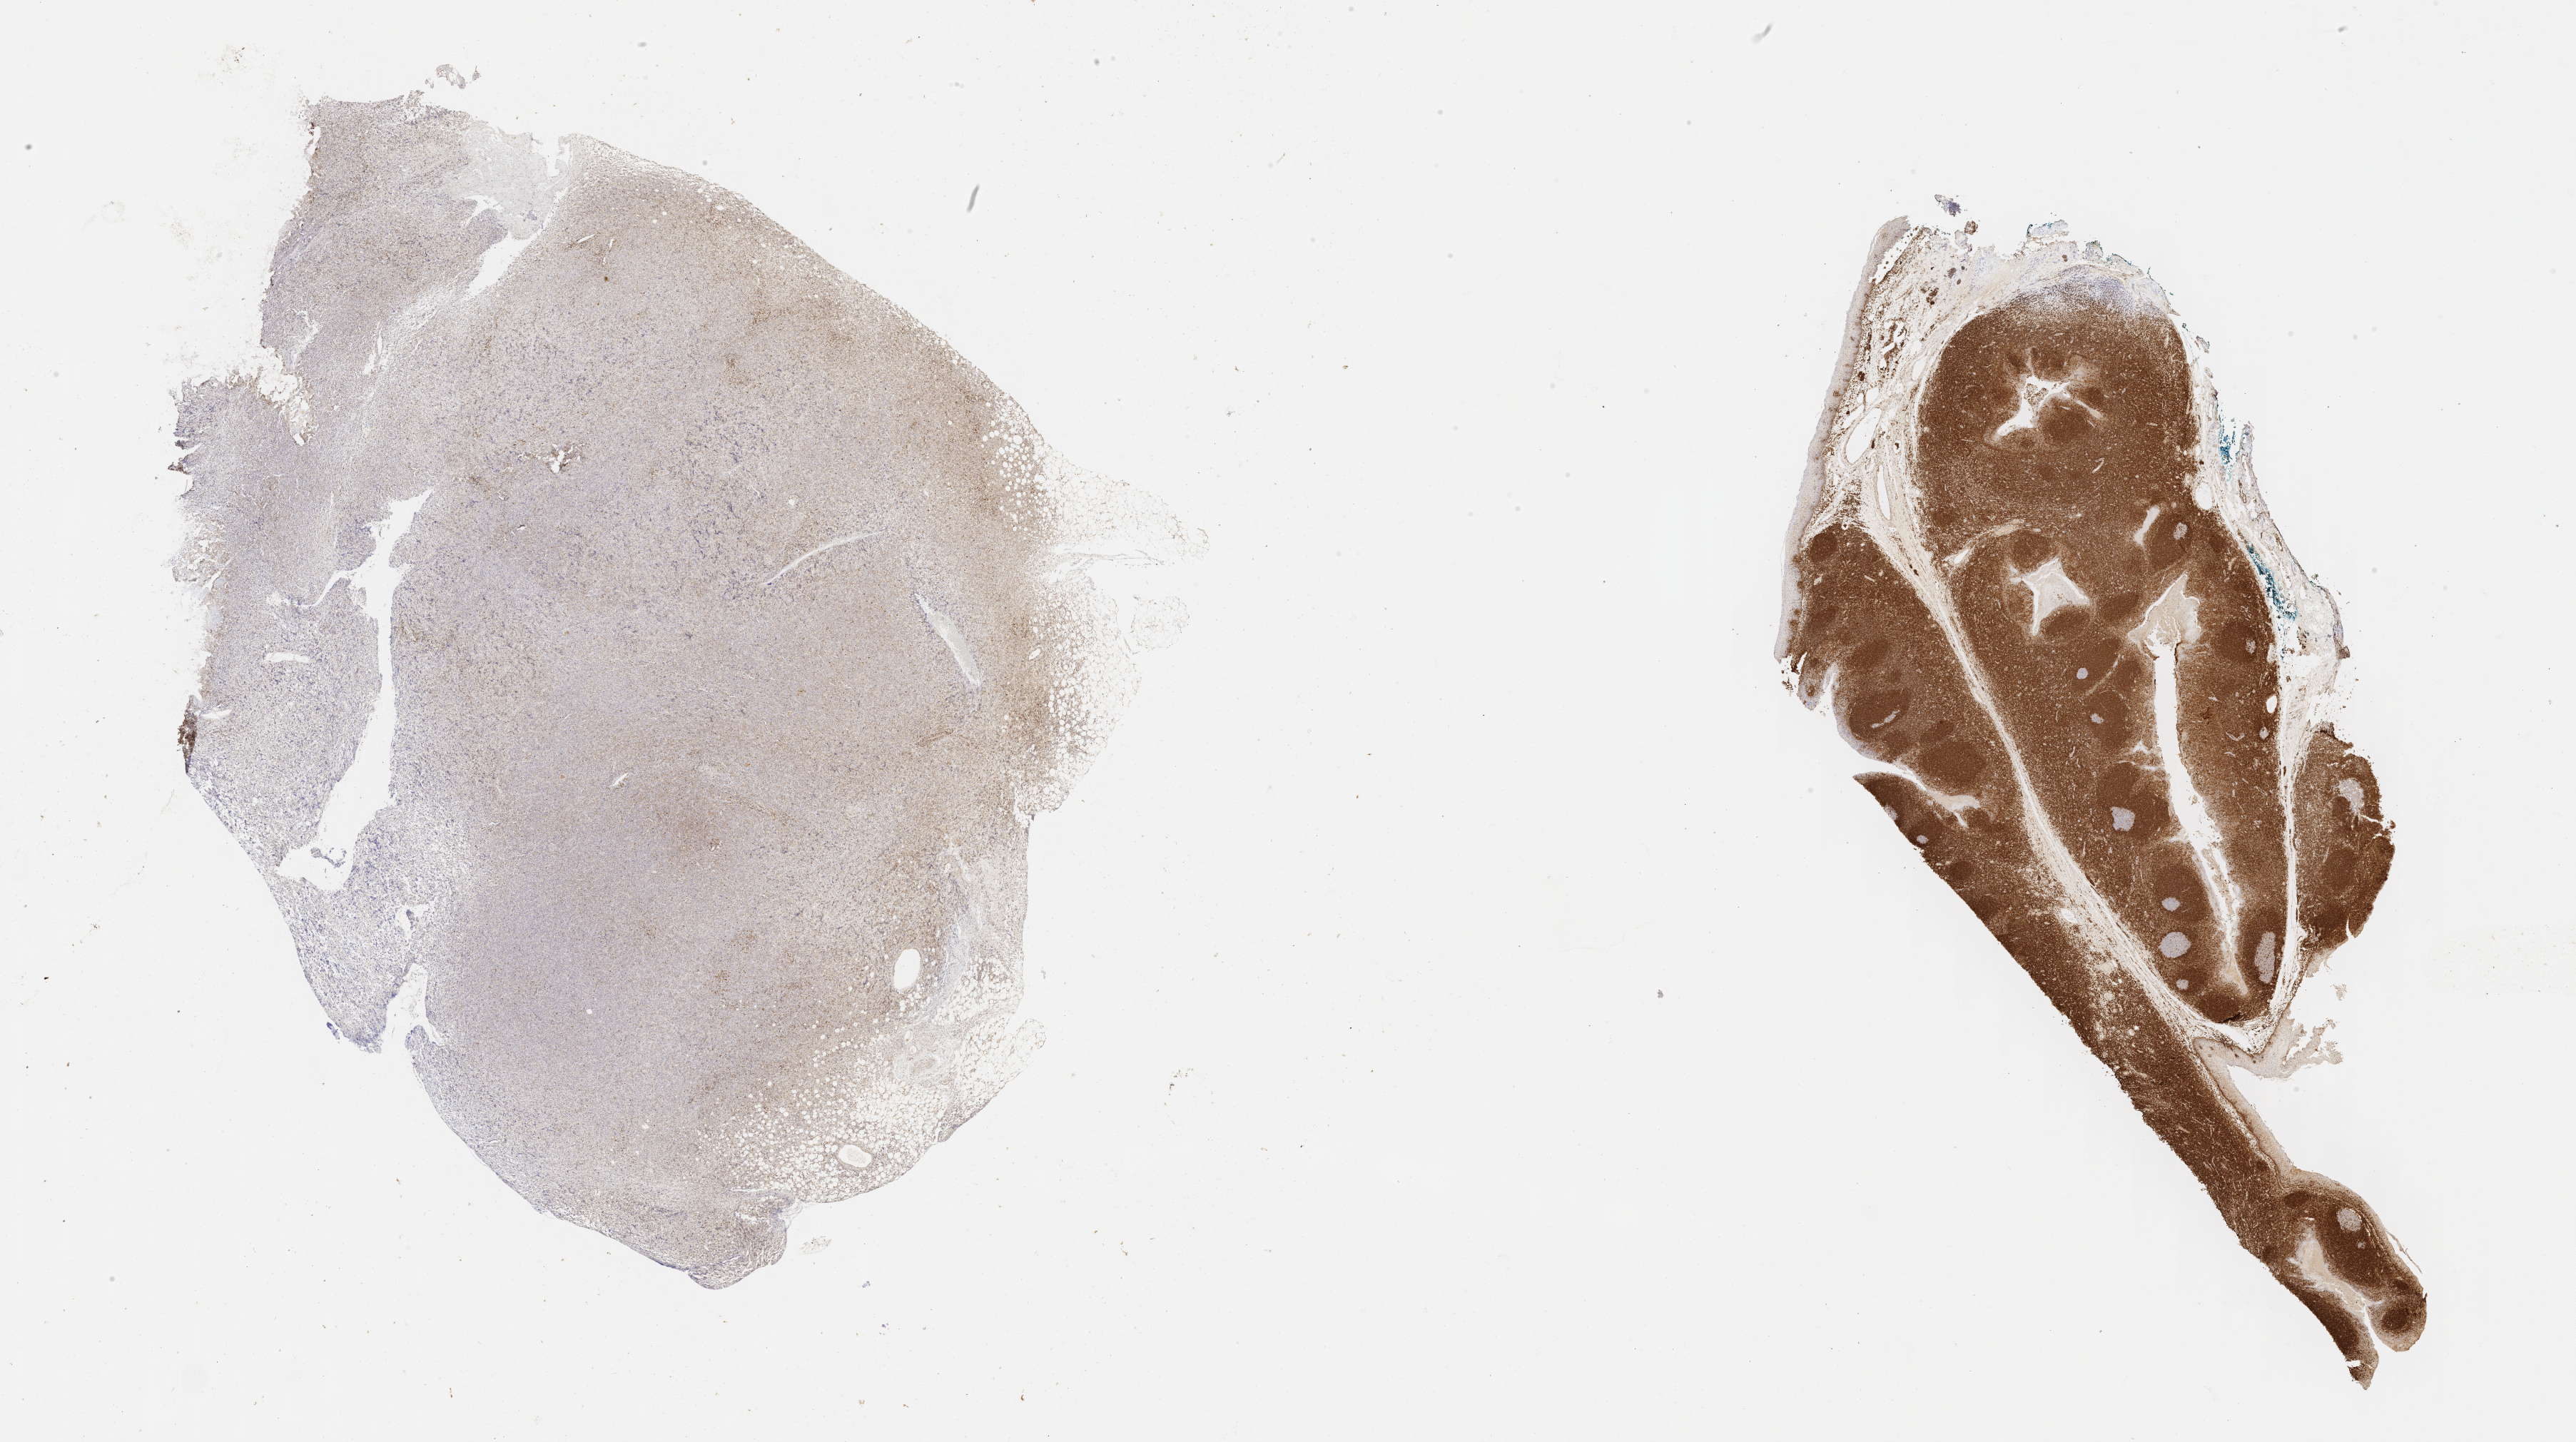
IHC for BCL2, whole-slide image, whole scanned area (about 29.2 x 16.3 mm) shown as a low-resolution overview. Patient sex: female.
- specimen: tumor tissue